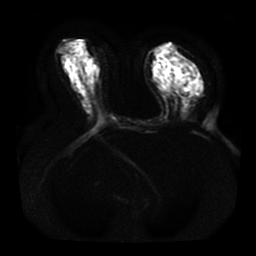
Breast MRI, one axial slice; slice 22 of 41 in the series (ordered by position); diffusion-weighted series; image 2 of 4 stored at this slice position (different b-values; order by instance number); 1.5 T; 5 mm slice thickness; 256 × 256 image matrix. Female patient.
Structures marked on this image (manually delineated by an expert):
- tumour on diffusion-weighted imaging: bounding box (x1, y1, x2, y2) in pixels: (180, 78, 199, 92)